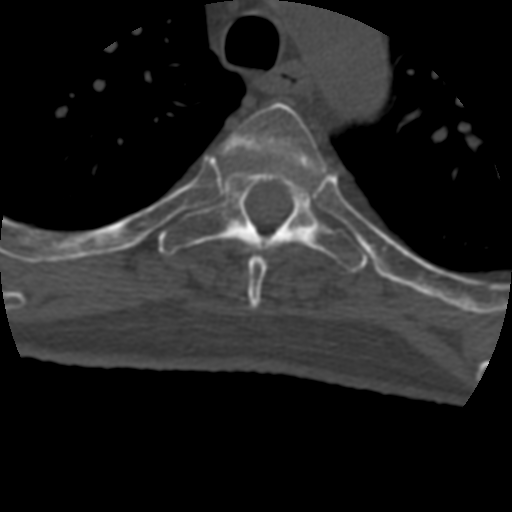
CT including the spine, one axial slice; position 326 of 399 along the scan axis; bone window (W 1800 / L 400 HU); 512 × 512 image matrix, field of view 160 × 160 mm. Patient age 69 years. Case-level facts recorded for this patient, not image findings: primary cancer: prostate.
Outlined on this slice (semi-automatic segmentation, software-assisted and operator-edited):
- T4 vertebra: bounding box [x1, y1, x2, y2] px = [223, 102, 326, 309]
- T5 vertebra: [158, 168, 368, 273]